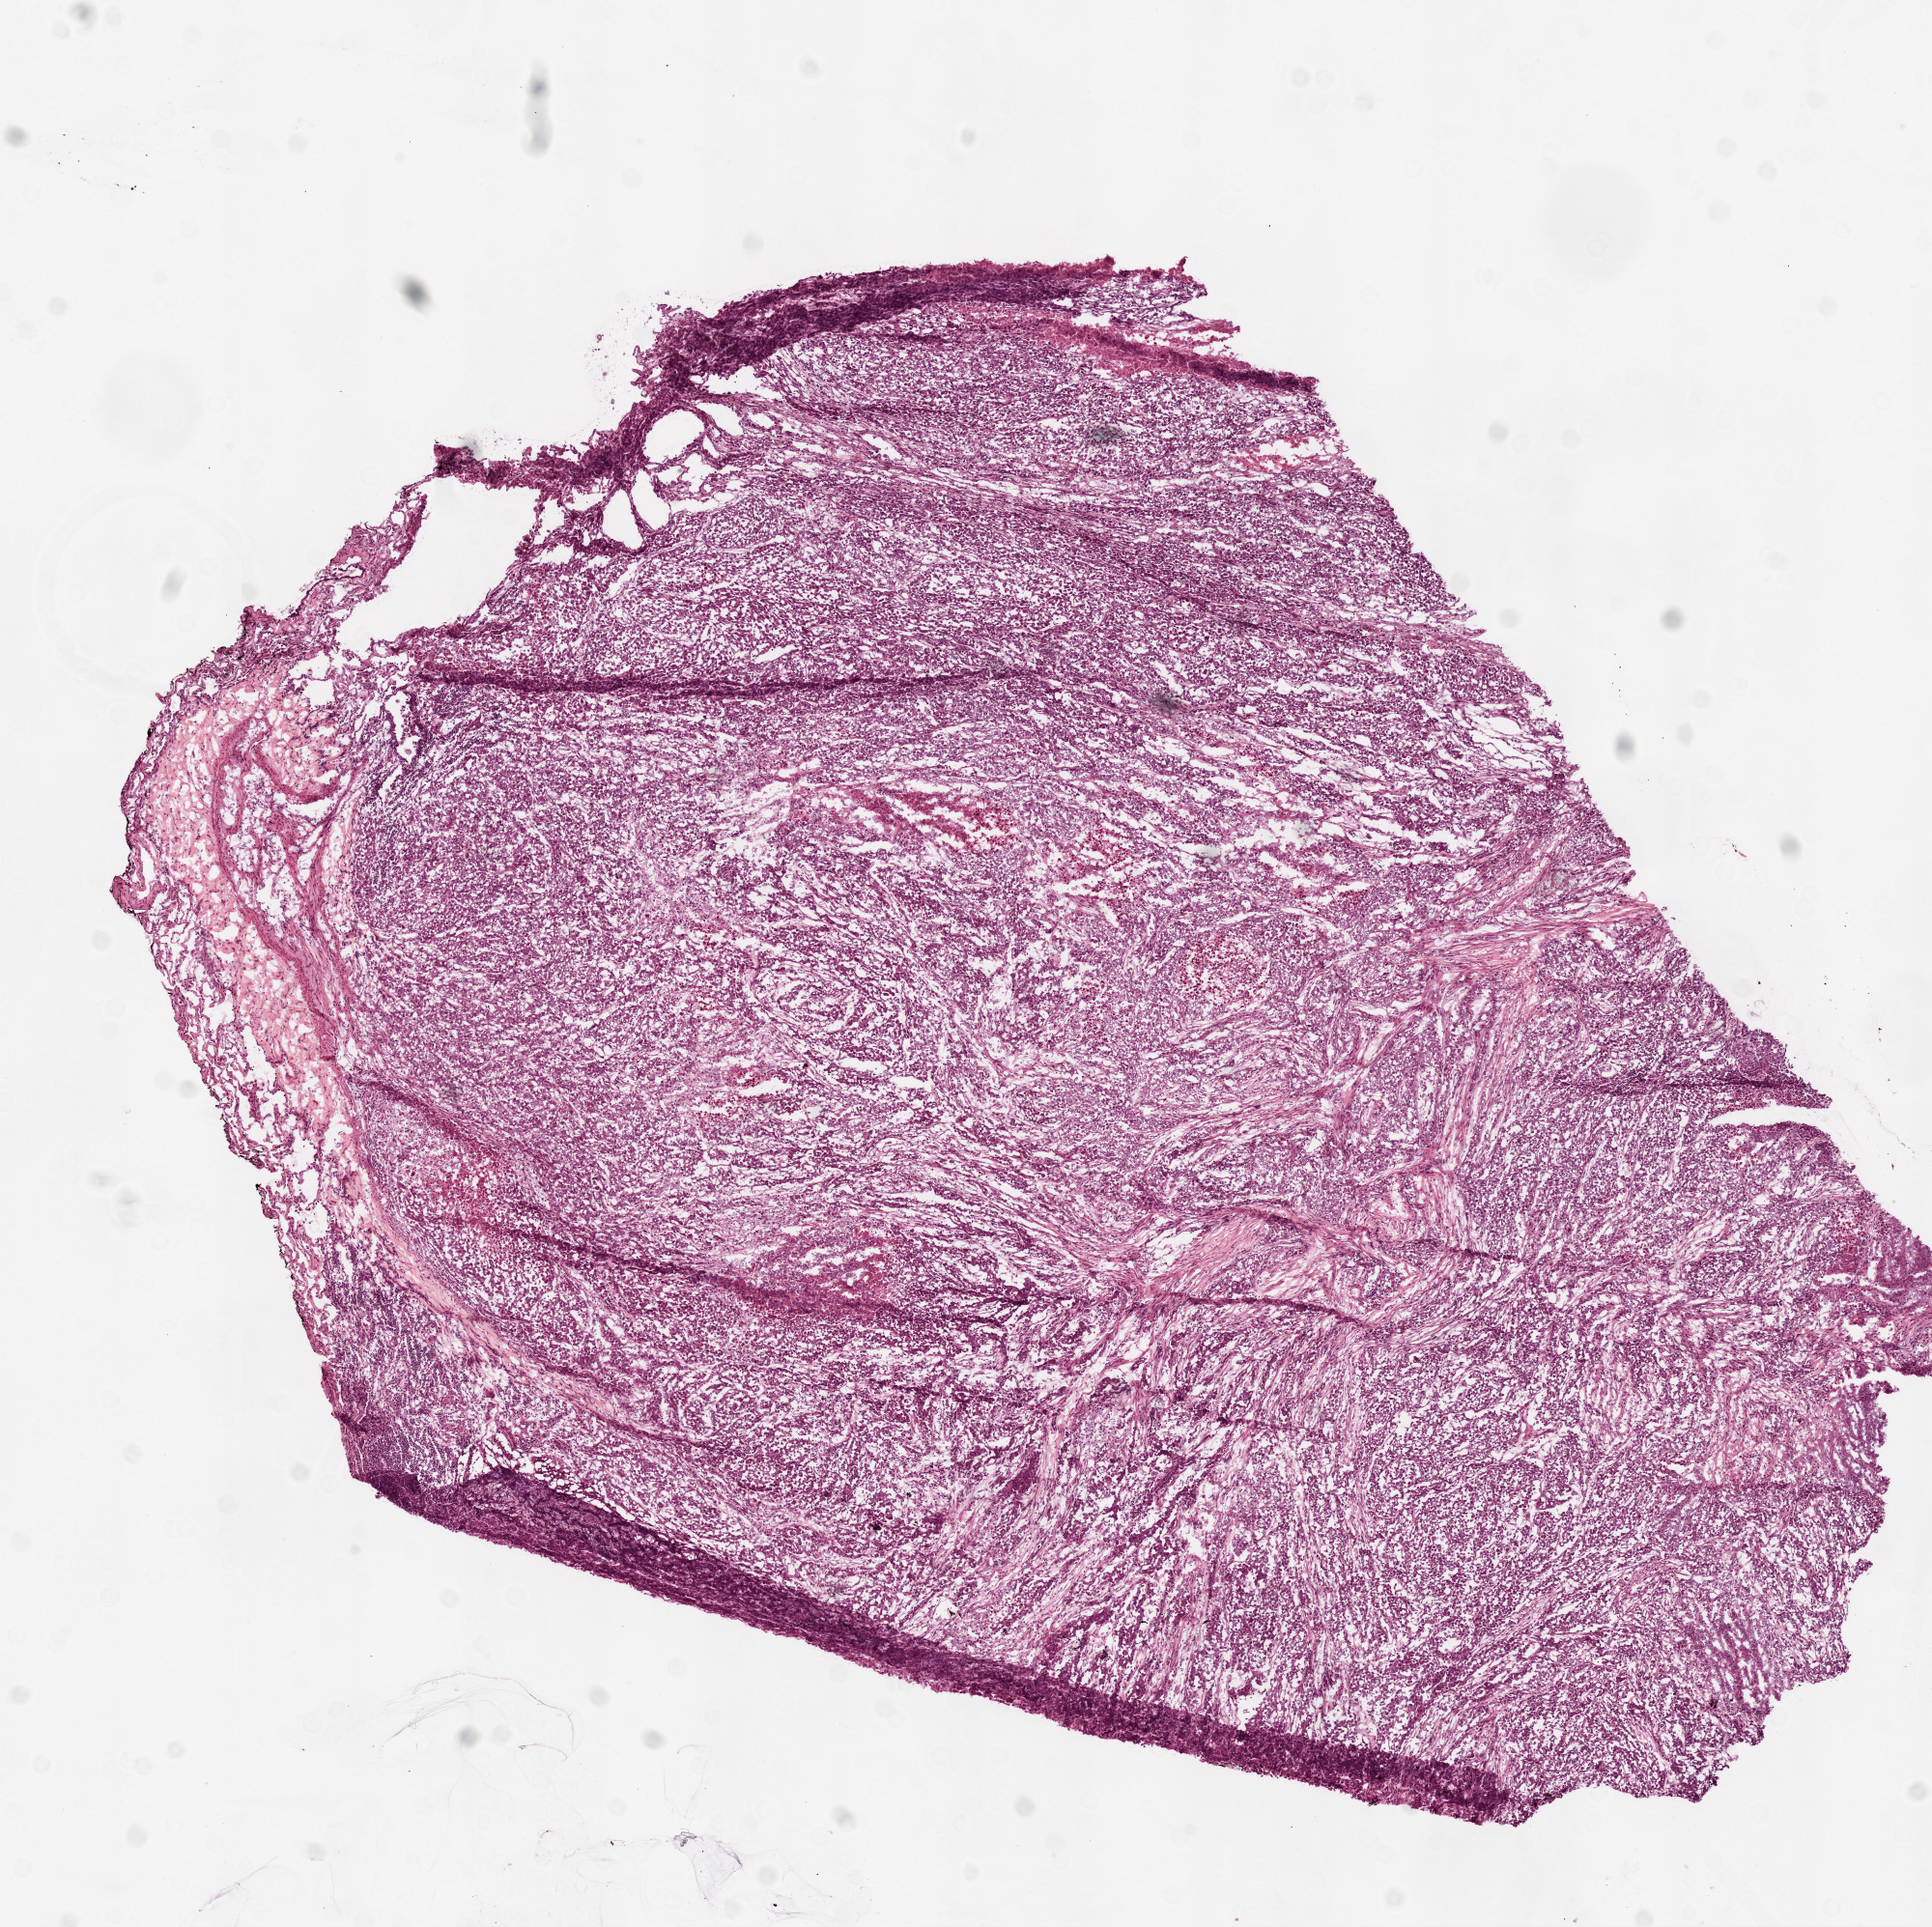
Whole-slide histology image, H&E — low-resolution overview of the scanned area, about 8.0 x 8.0 mm; frozen section from the top of the tissue portion; primary tumour sample from the lung. Patient: female, age at initial diagnosis 52 years. Composition of this section per pathologist review: tumour cells 85%, tumour nuclei 90%, normal cells 5%, stromal cells 5%, necrosis 5%.
Diagnosis: Adenocarcinoma, NOS (upper lobe, lung). AJCC pathologic stage: IV. Laterality: right.